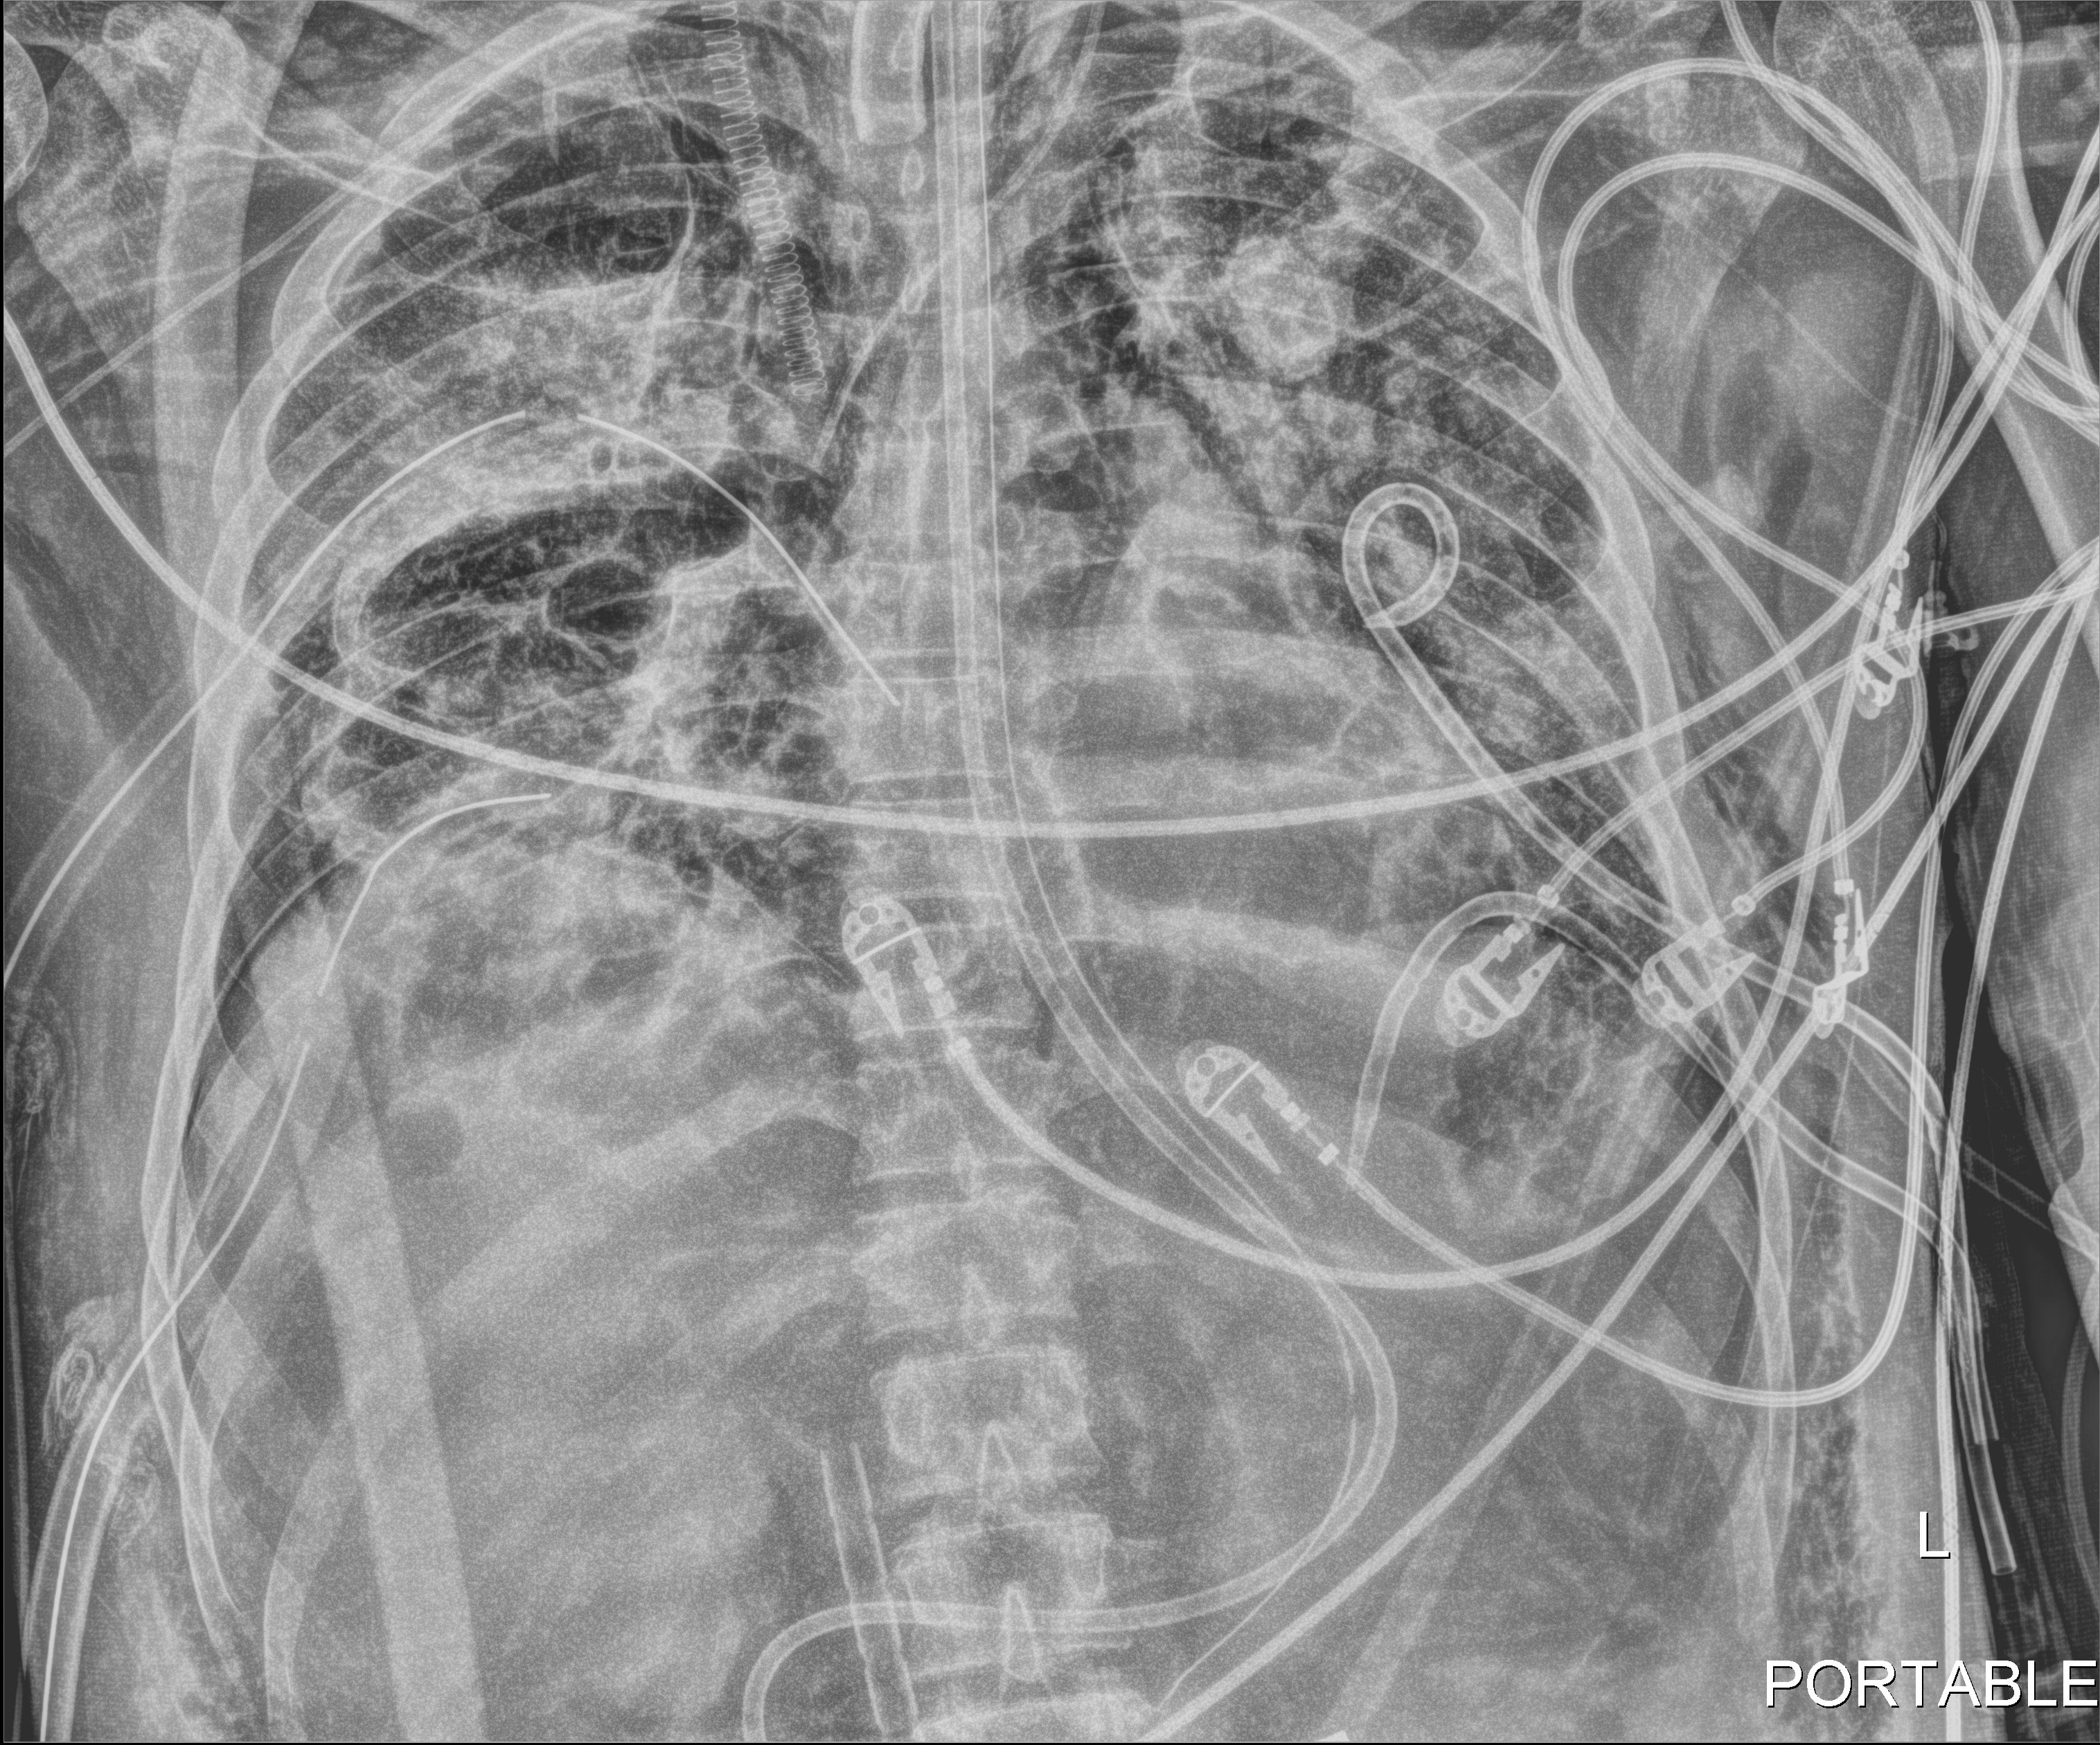
Chest X-ray. Adult patient hospitalised with COVID-19, age 18–59 years.
From the hospital-stay record, not from the radiograph (when in the stay this image was taken is not recorded): mechanically ventilated during this hospital stay: yes; admitted to intensive care during this hospital stay: yes.